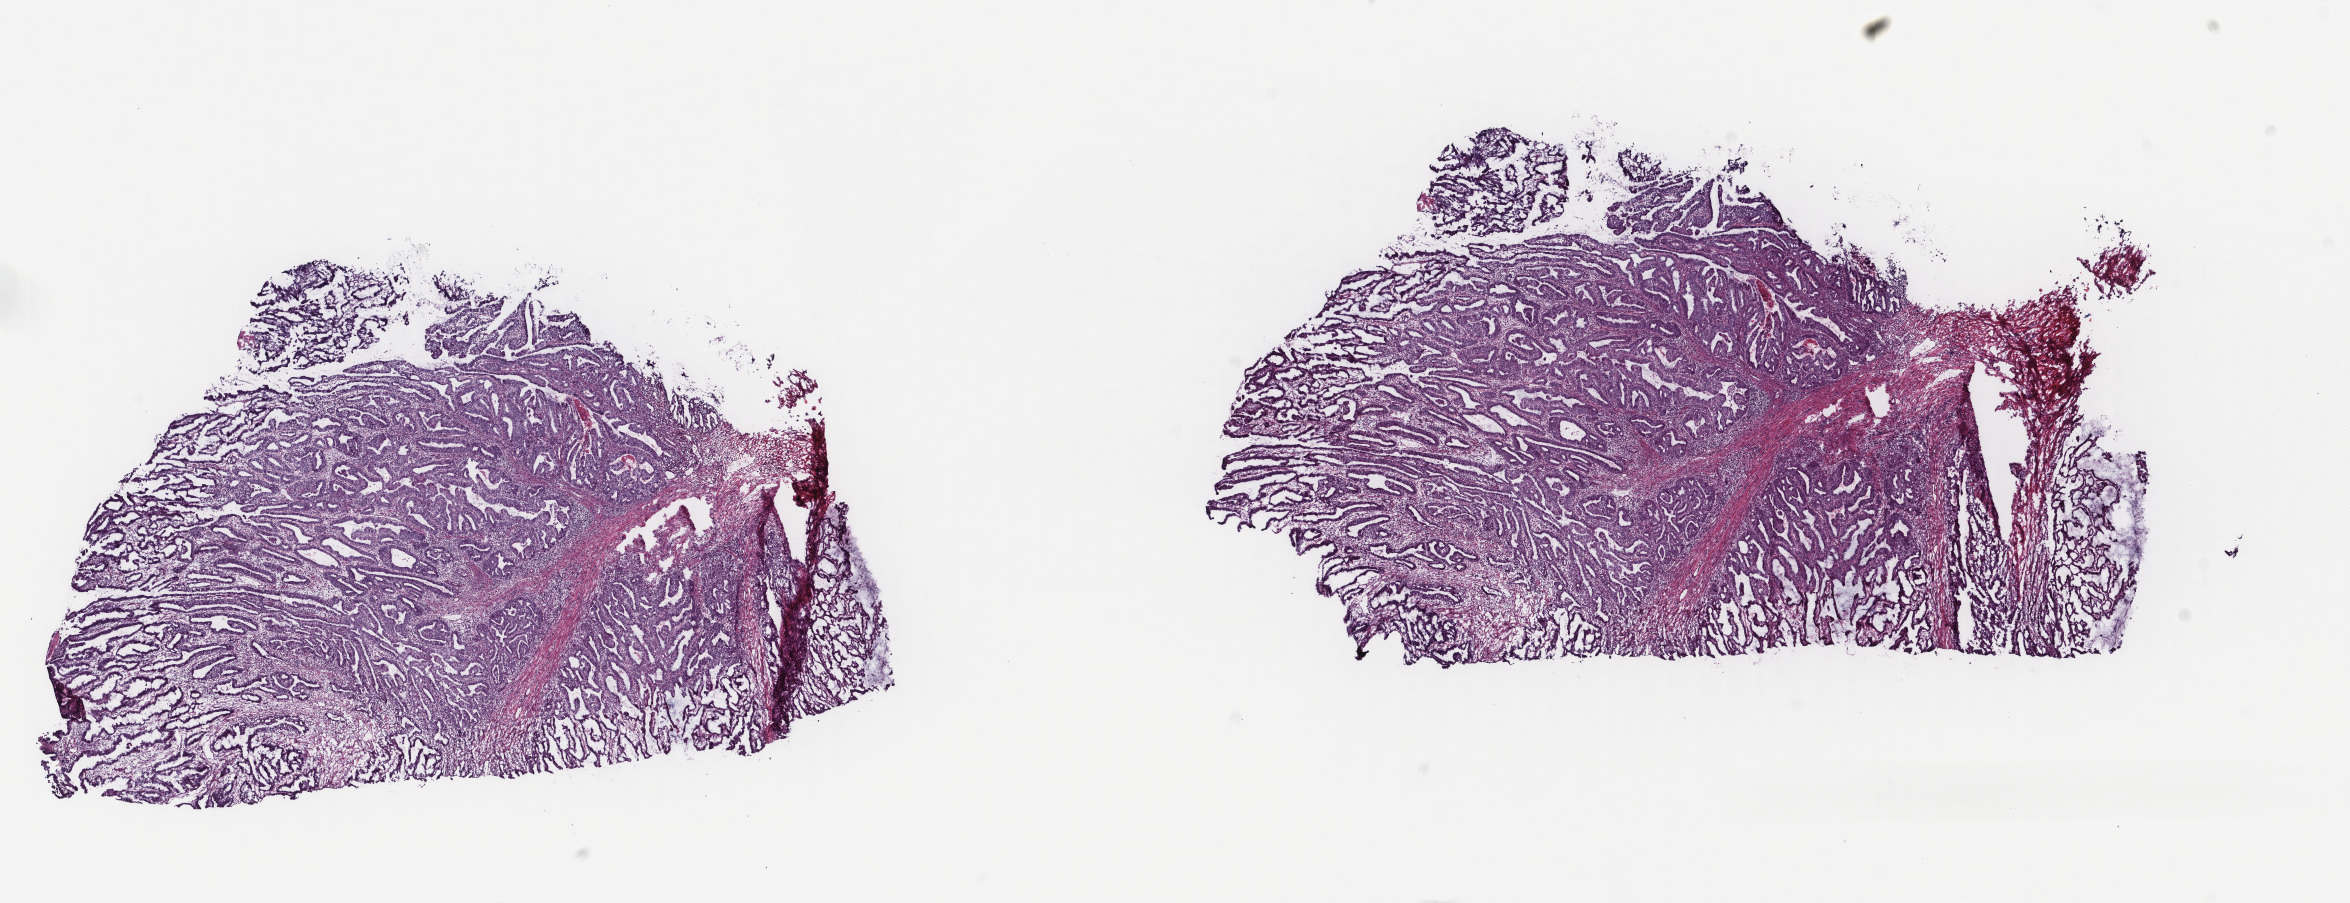
H&E-stained whole-slide image — shown as a low-resolution overview of the whole scanned area (about 18.7 x 7.2 mm, acquisition: 40x scan). Frozen section from the top of the tissue portion. Sample: primary tumour, uterus. Patient: female, age at initial diagnosis 50 years. Histologic grade: G2 (moderately differentiated). Pathologist review of this section (percent, as recorded): tumour cells 90%, tumour nuclei 60%, normal cells 10%, stromal cells 0%, necrosis 0%. Infiltration values recorded for this section: lymphocyte infiltration 0%, monocyte infiltration 0%, neutrophil infiltration 0%.
FIGO stage: IIIC. Diagnosis: Endometrioid adenocarcinoma, NOS (endometrium).